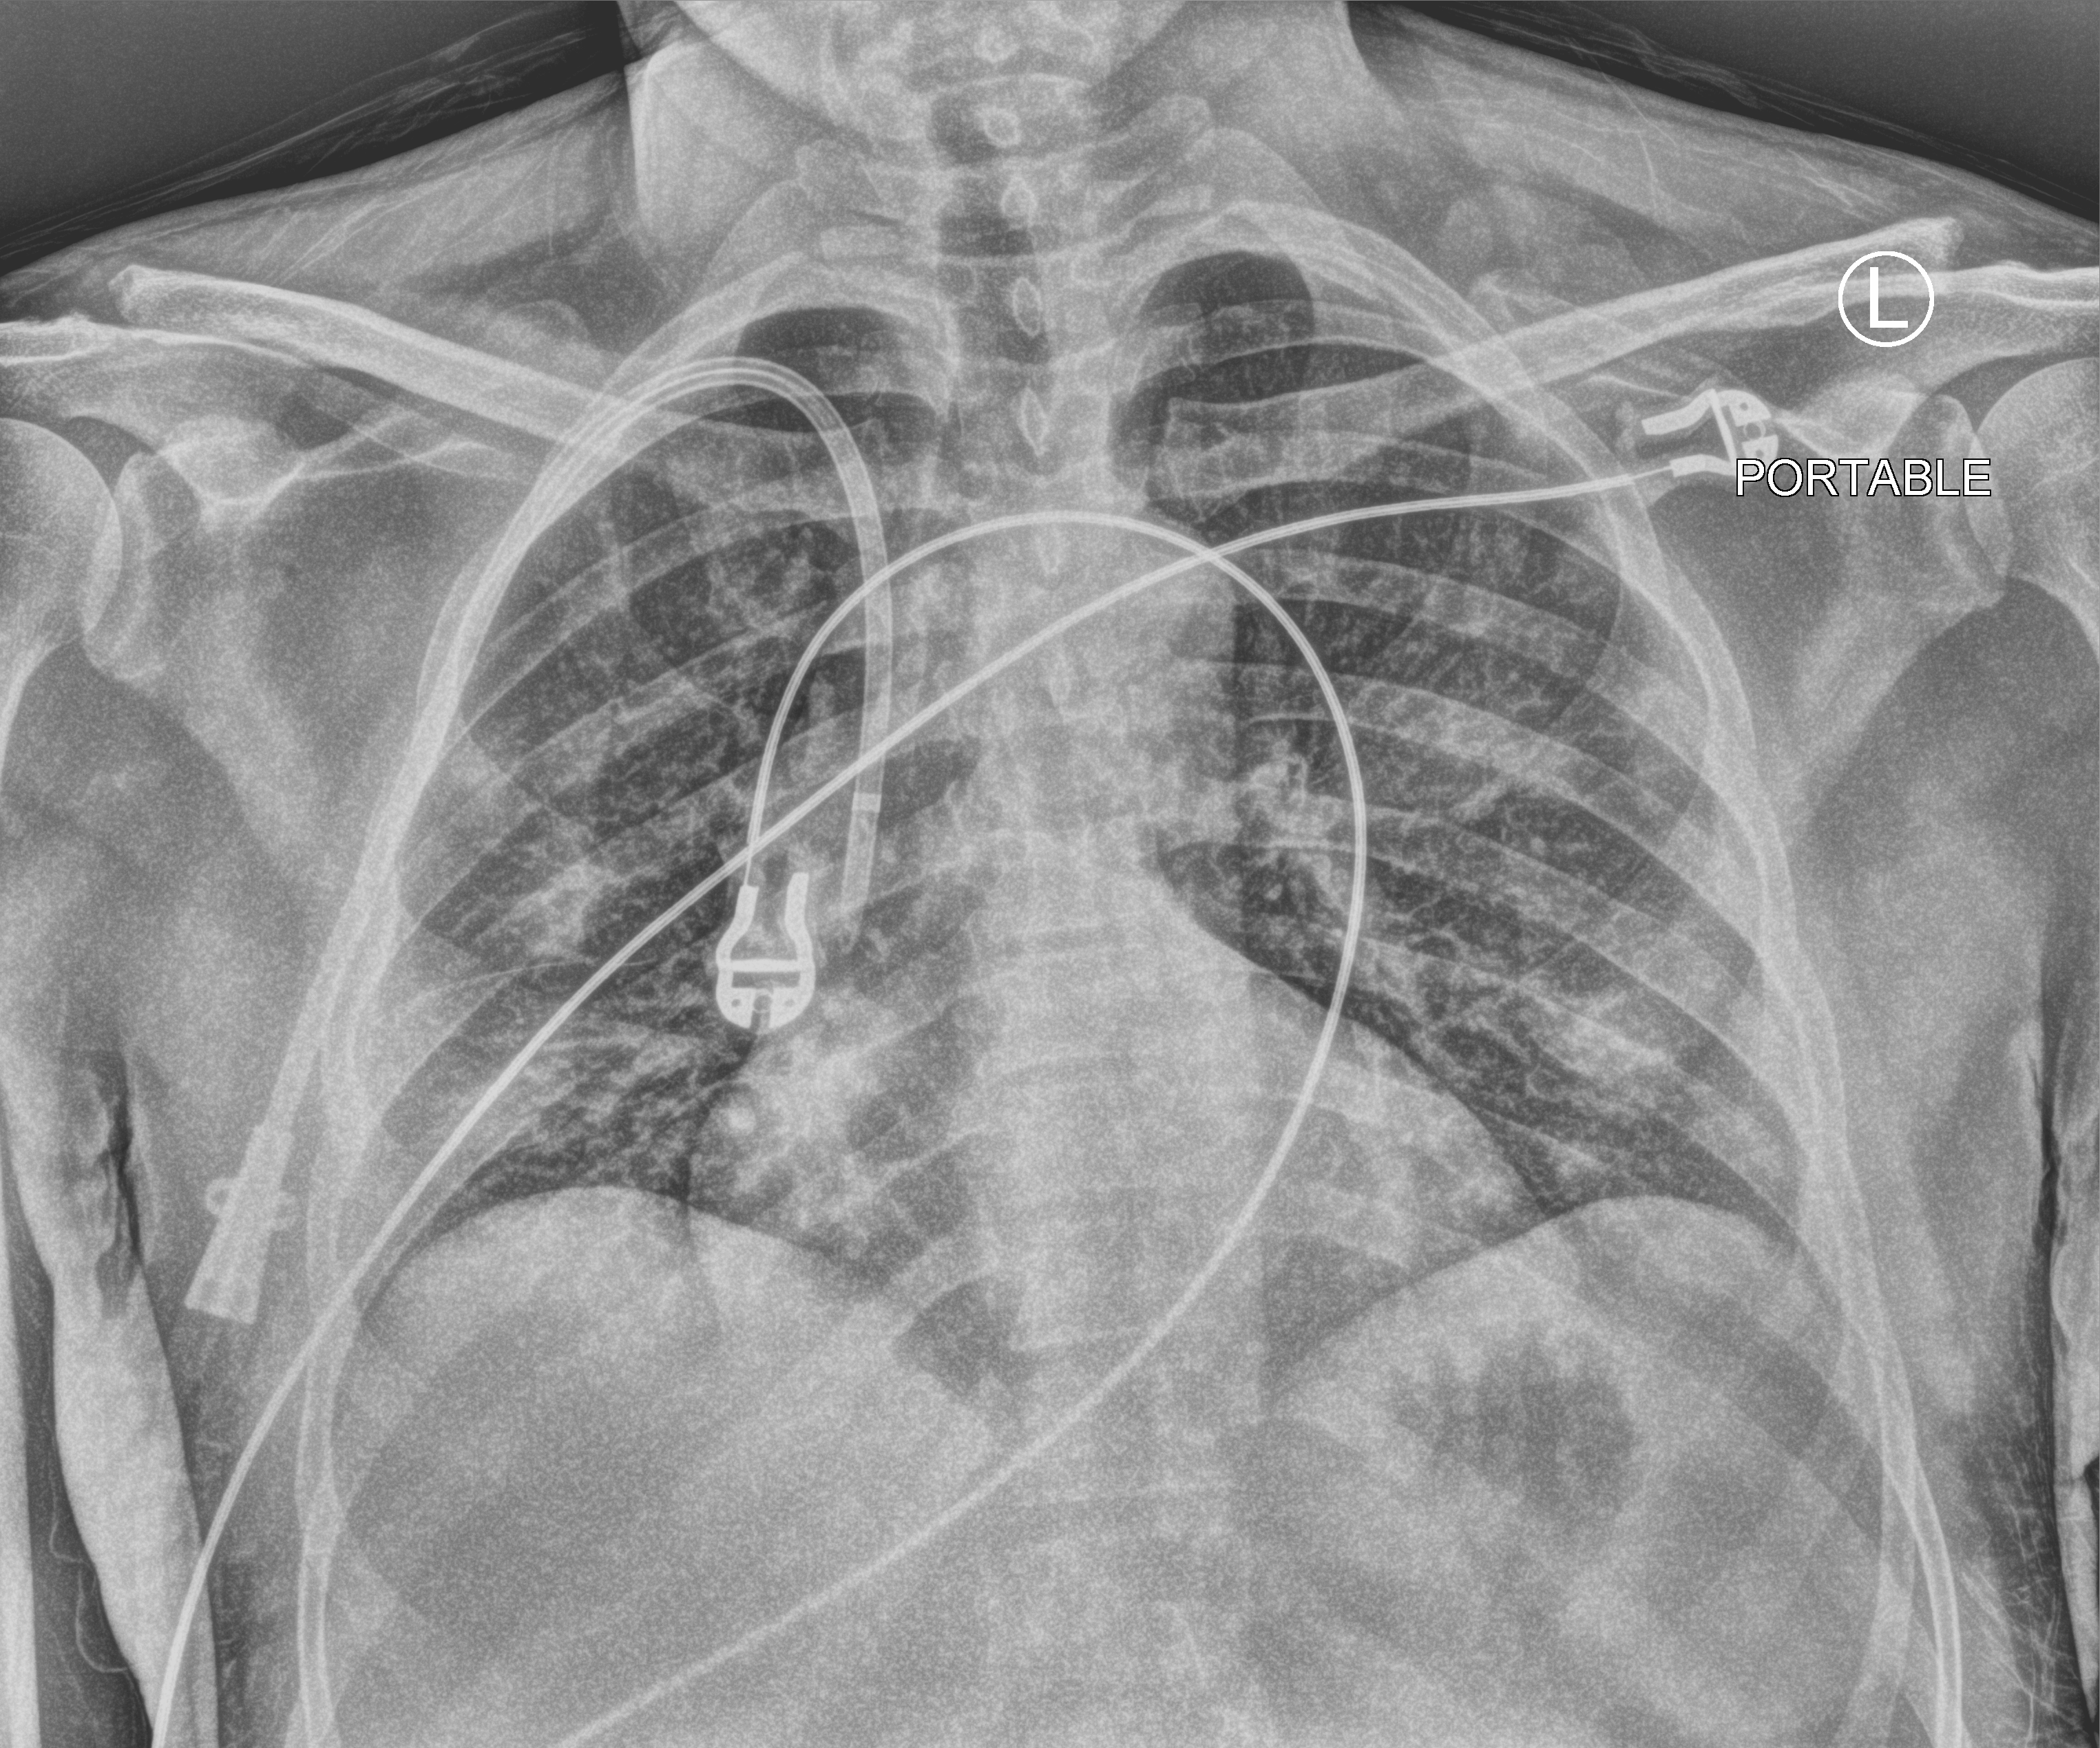
Portable chest radiograph. Male patient hospitalised with COVID-19, age 18–59 years.
Hospital-stay facts (about this admission, not read from this image; timing relative to this image not recorded):
- mechanically ventilated during this hospital stay: no